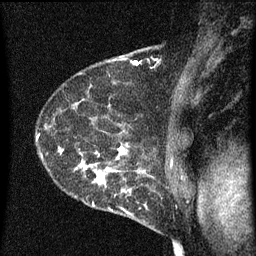
Breast MRI (dynamic contrast-enhanced), one sagittal slice; slice 47 of 60 in the series (ordered by position); dynamic contrast-enhanced series, image 2 of 3 at this slice position (ordered by acquisition); 1.5 T; TE 4.2 ms, TR 8 ms; 2 mm slice thickness; 256 × 256 image matrix, field of view 180 × 180 mm. Female patient, age 54 years.
Structures marked on this image (semi-automatic segmentation, software-assisted and operator-edited):
- analysis volume of interest (the breast-tissue region the enhancement analysis was run in; not a lesion): bounding box (x1, y1, x2, y2) in pixels: (49, 138, 164, 209)
- tumour enhancement mask (voxels above the 70 % enhancement threshold inside the analysis volume of interest): (59, 142, 149, 209)